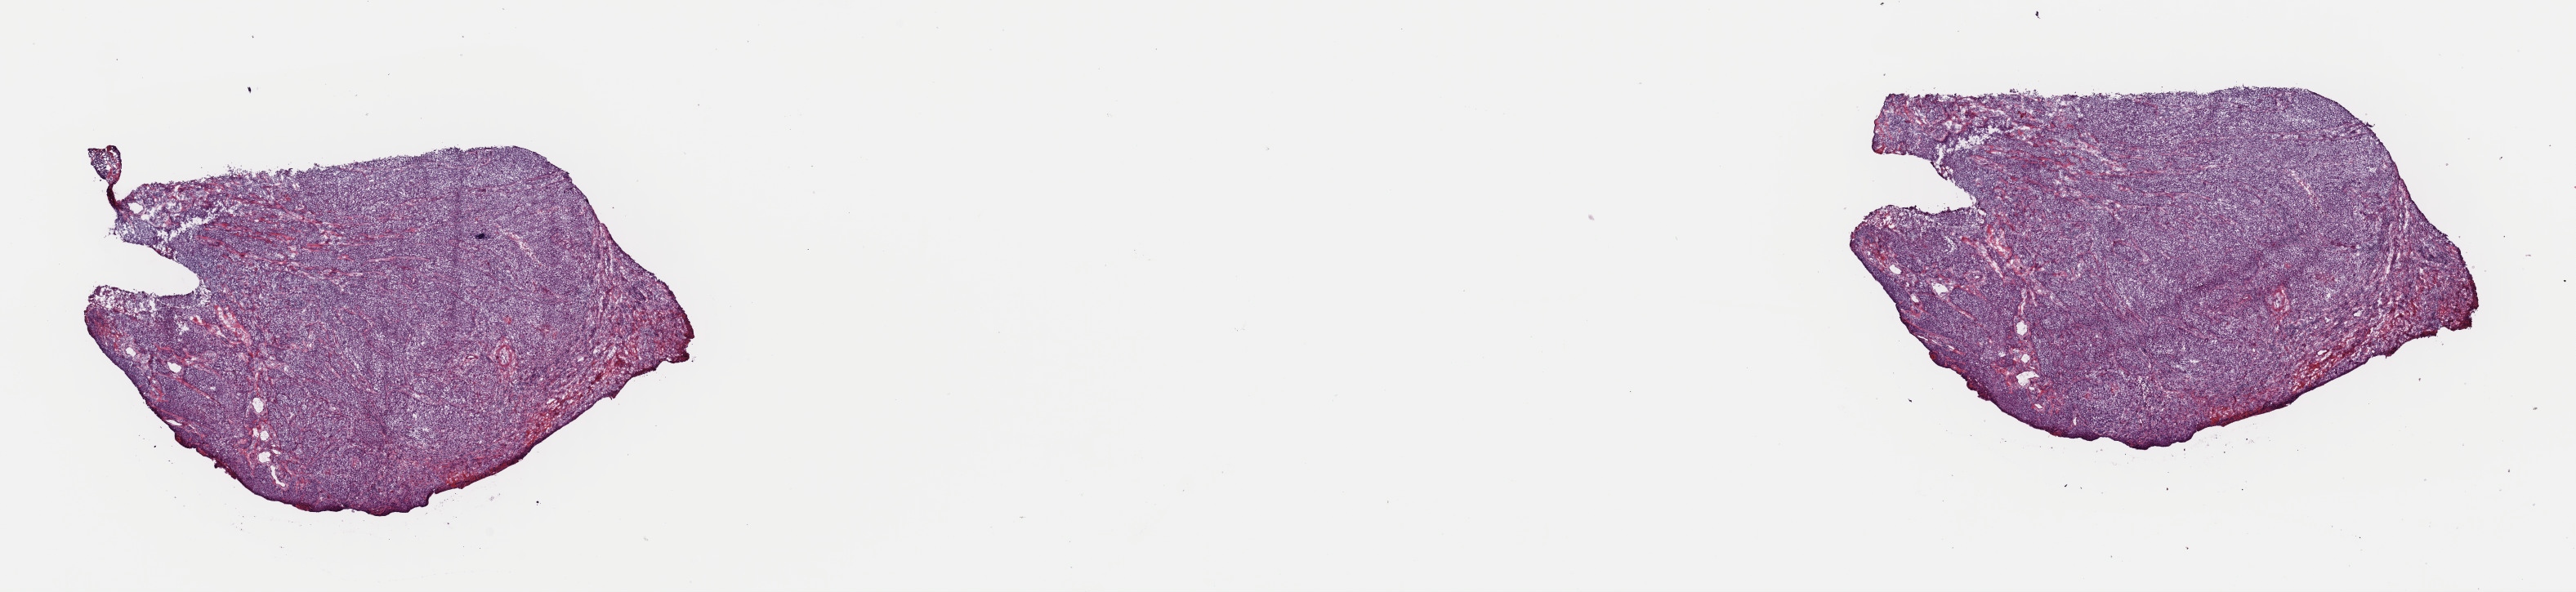
Digitized Hematoxylin and eosin (H&E) stained tissue section (whole slide), shown as a low-resolution overview of the whole scanned area (about 24.9 x 5.7 mm, acquisition: 40x scan); frozen section from the top of the tissue portion; head and neck, primary tumour sample. Male, age 71 years at initial diagnosis. Histologic grade: G3 (poorly differentiated). Slide review estimates, as recorded: tumour cells 100%, tumour nuclei 70%, normal cells 0%, stromal cells 0%, necrosis 0%. Infiltration values recorded for this section: lymphocyte infiltration 15%, monocyte infiltration 0%, neutrophil infiltration 0%.
AJCC pathologic stage: III (7th edition). Diagnosis: Squamous cell carcinoma, NOS (cheek mucosa). Laterality: left.